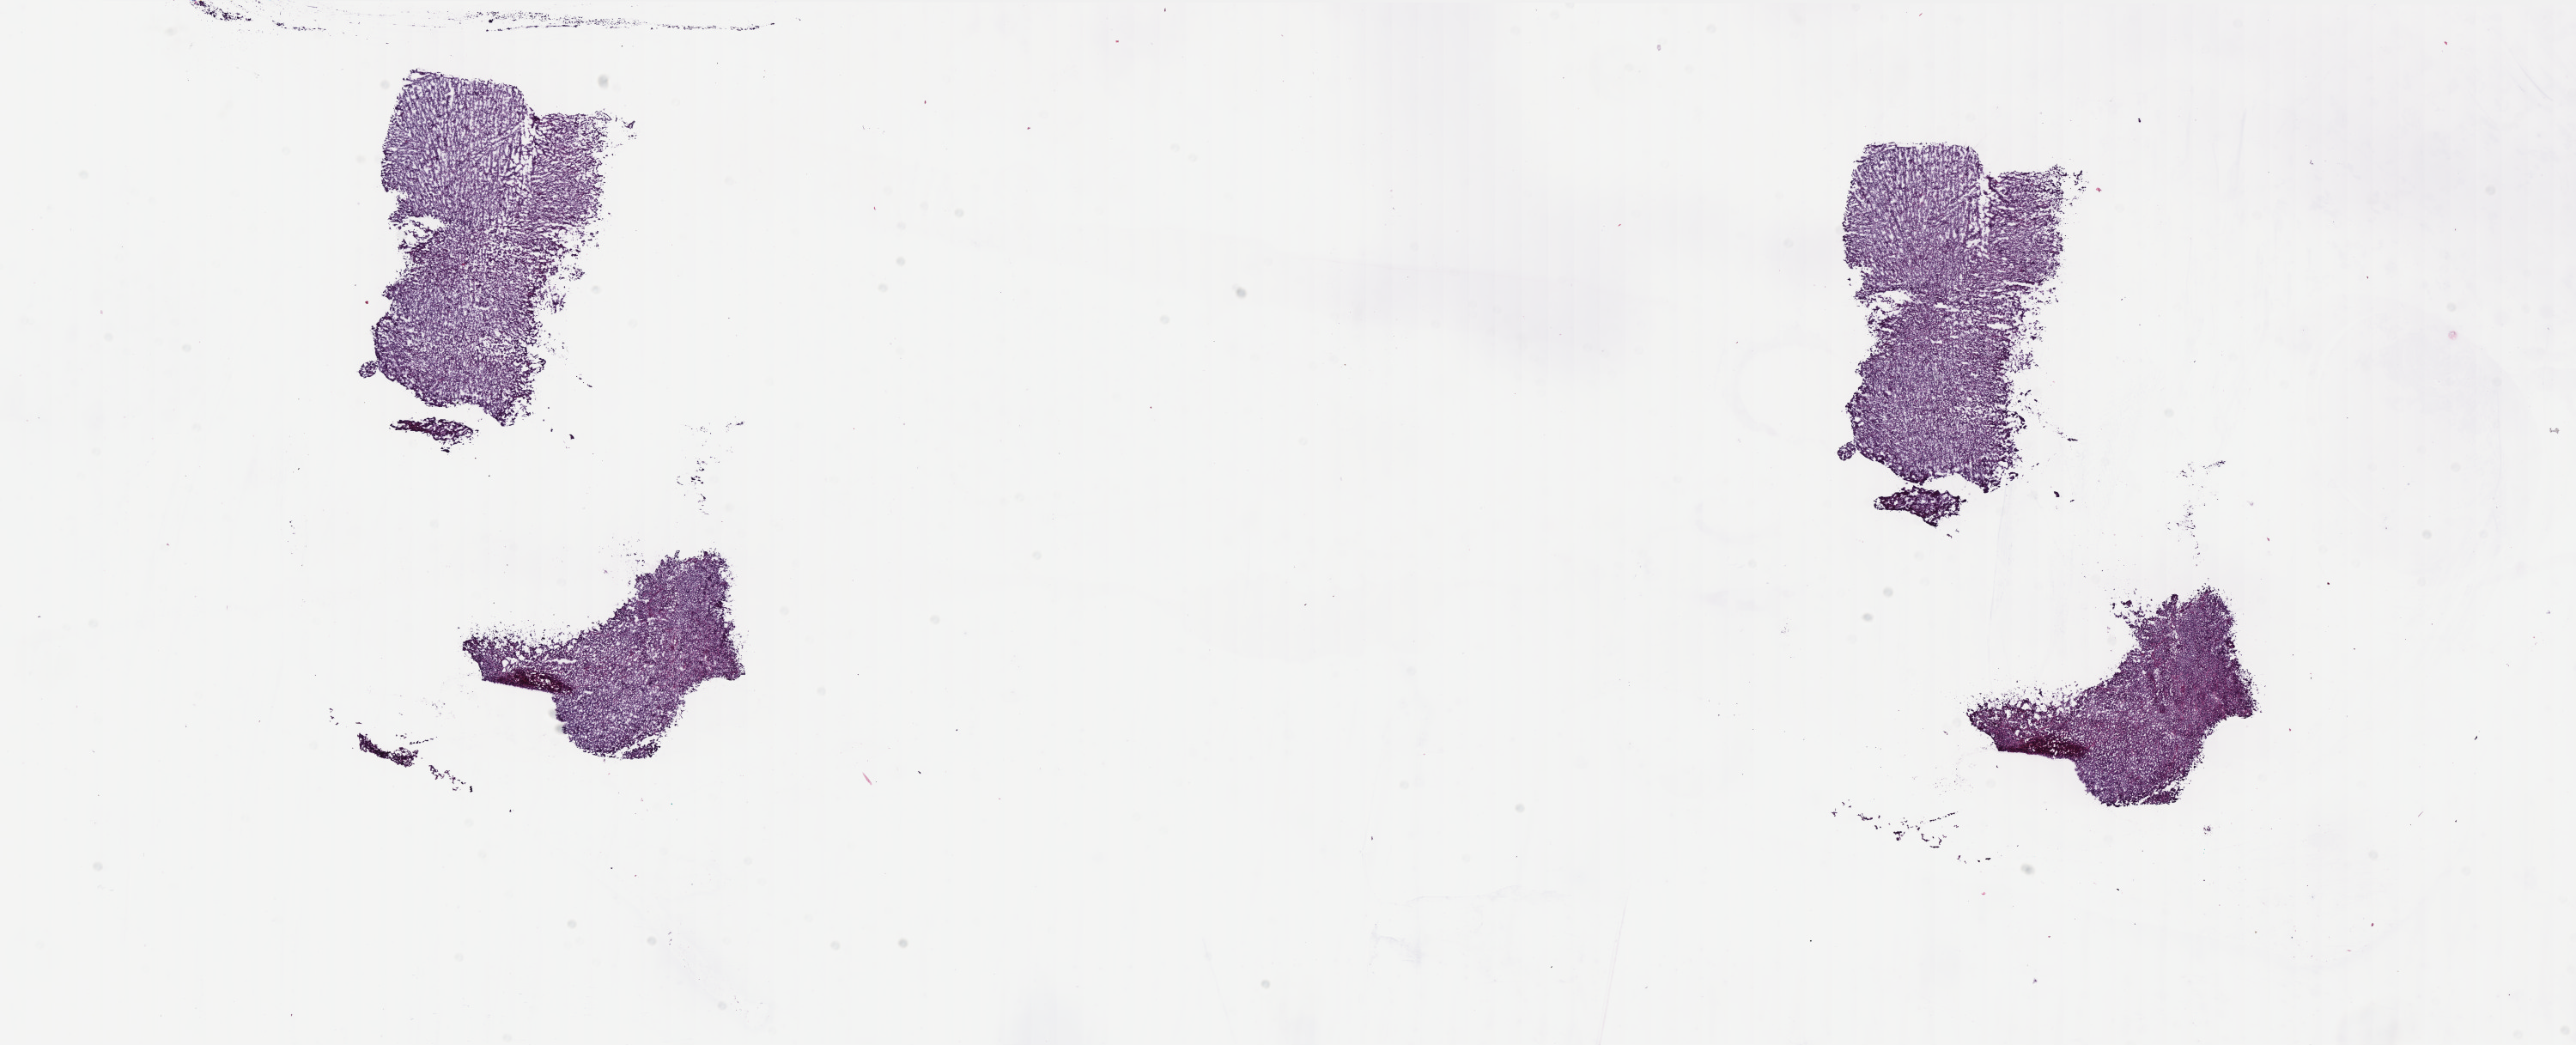
Hematoxylin and eosin (H&E) stained whole-slide image — low-resolution overview of the scanned area, about 24.1 x 9.8 mm. Frozen section from the bottom of the tissue portion. Uterus, primary tumour sample. Female, age 69 years at initial diagnosis. Histologic grade: G3 (poorly differentiated). Slide review estimates, as recorded: tumour cells 98%, tumour nuclei 50%, normal cells 0%, stromal cells 1%, necrosis 1%. Inflammatory infiltration, as recorded: lymphocyte infiltration 40%, monocyte infiltration 0%, neutrophil infiltration 0%.
Histologic diagnosis: Endometrioid adenocarcinoma, NOS (endometrium). Lymph nodes positive (case pathology): 0 of 13 examined. FIGO stage: IA.